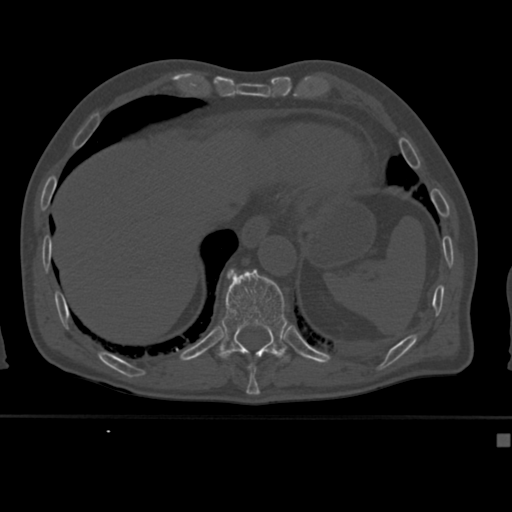
CT including the spine, one axial slice. Slice 215 of 430 in the series (ordered by position). Reconstruction kernel Br40s. Bone window (W 1800 / L 400 HU). 1.5 mm slice thickness. 512 × 512 image matrix, field of view 337 × 337 mm. Patient: male, 64 years. From the clinical record (not read from this slice): primary cancer: uterus; vertebrae with lytic lesions (as recorded): T1, T4, T5, T7, L5.
Outlined on this slice (semi-automatically segmented with operator editing):
- T10 vertebra: bounding box <247,364,256,382> (left, top, right, bottom; pixels)
- T11 vertebra: <218,269,289,362>